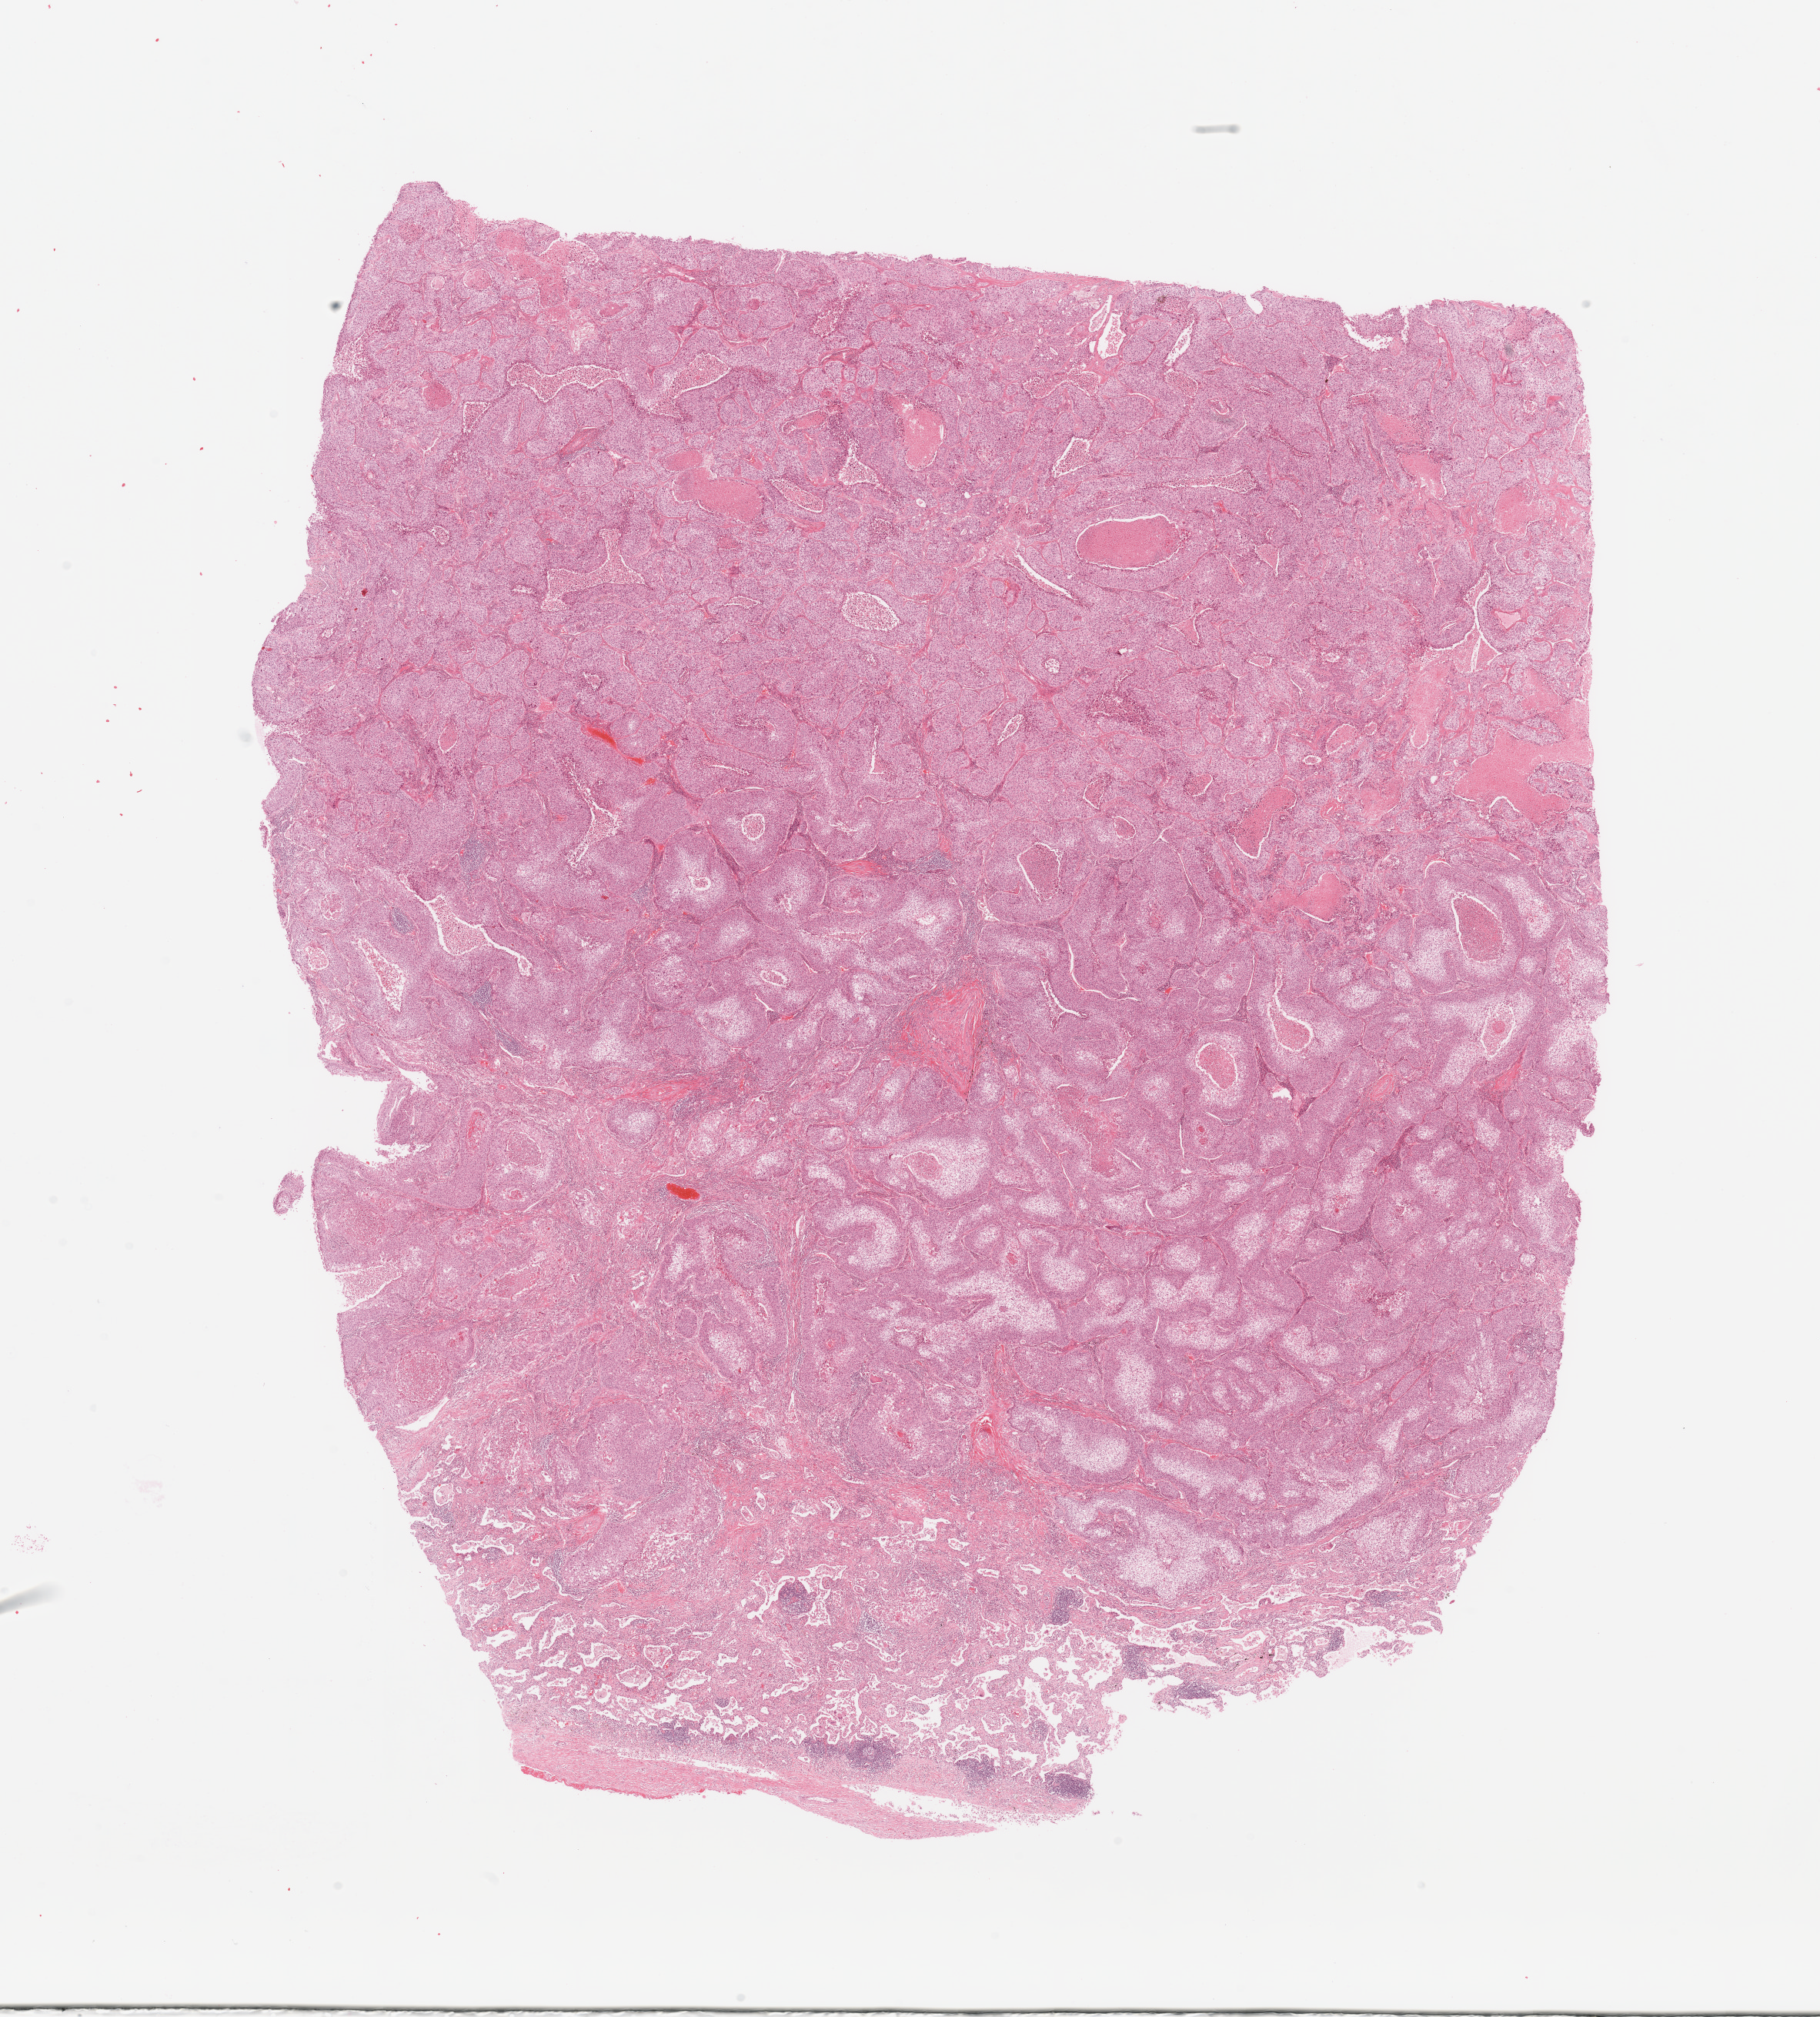
Whole-slide histology image, H&E, shown as a low-resolution overview of the whole scanned area (about 18.7 x 20.7 mm, acquisition: 20x scan). Lung, tumour tissue. 59-year-old male patient. Histologic grade: G2 (moderately differentiated).
• histologic diagnosis: Squamous cell carcinoma, NOS
• AJCC pathologic stage: IIB